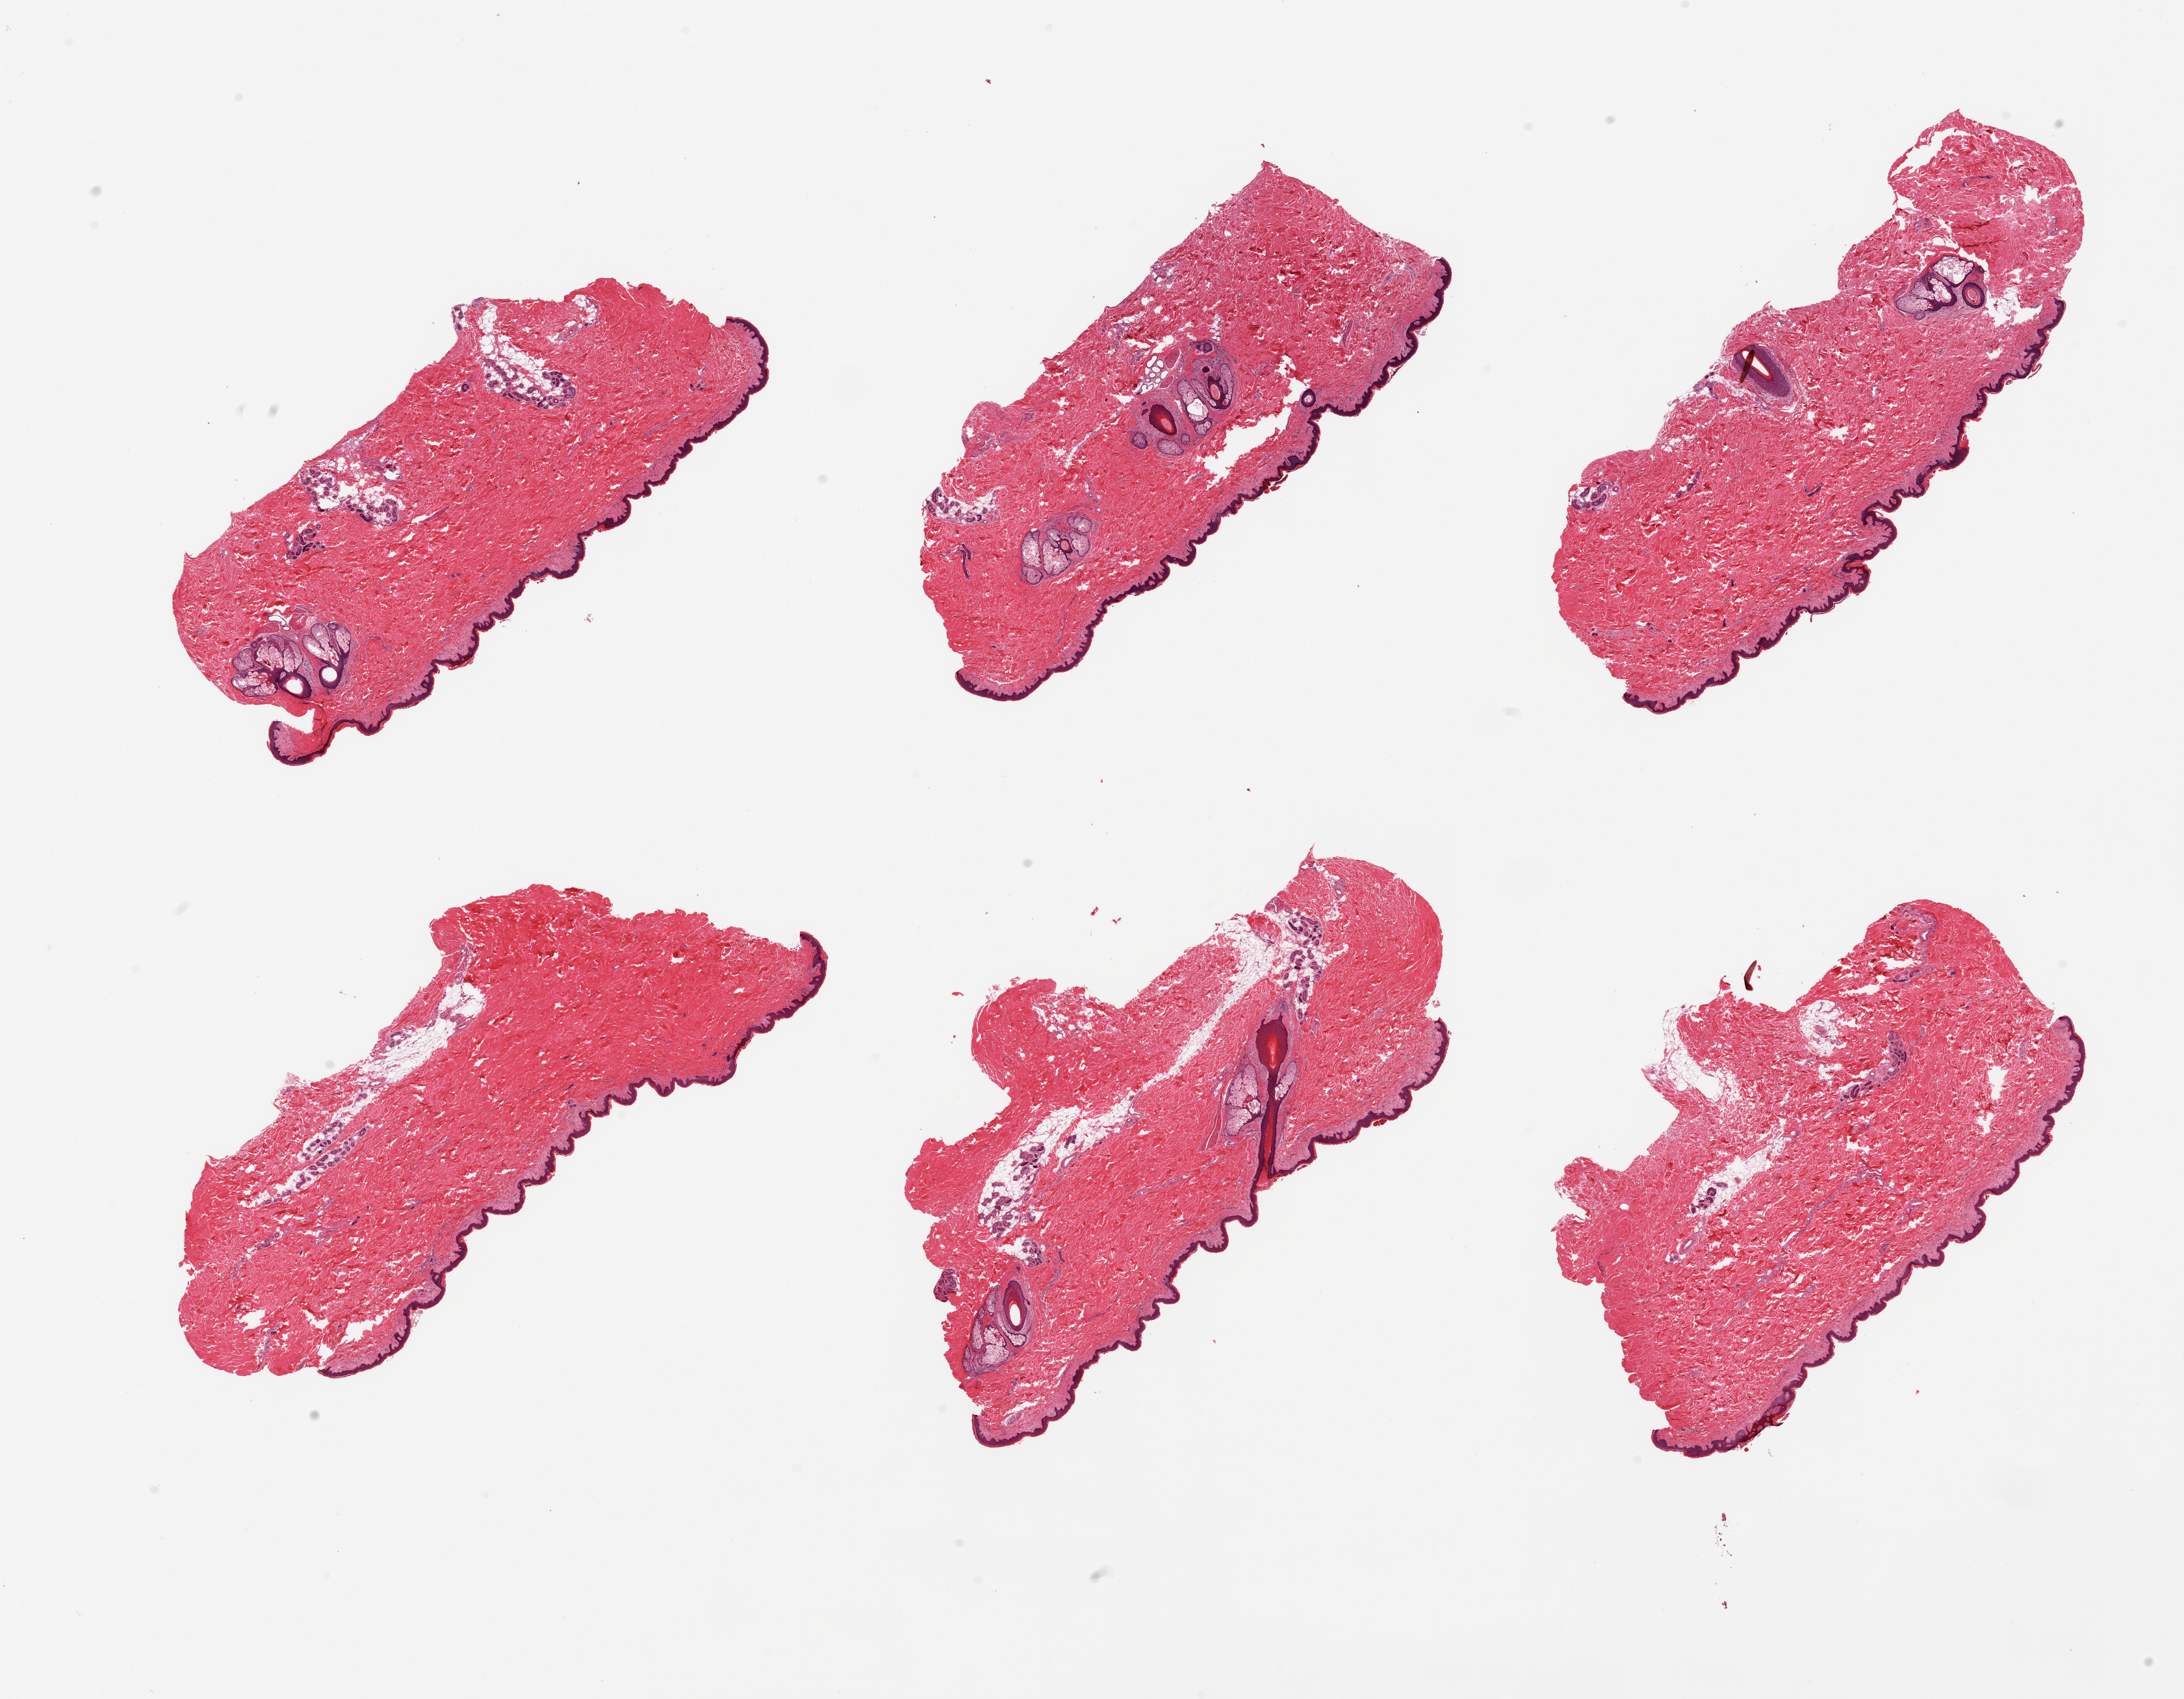
Haematoxylin and eosin whole-slide image, brightfield, shown as a low-resolution overview of the whole scanned area (about 26.6 x 20.7 mm), PAXgene-fixed paraffin-embedded (PFPE) section, section of skin of suprapubic region (target tissue), tissue donor sample. Donor: male.
Reviewer comment on this tissue sample: 6 pieces, minimal dermal fat; squamous epithelium is ~50 microns.